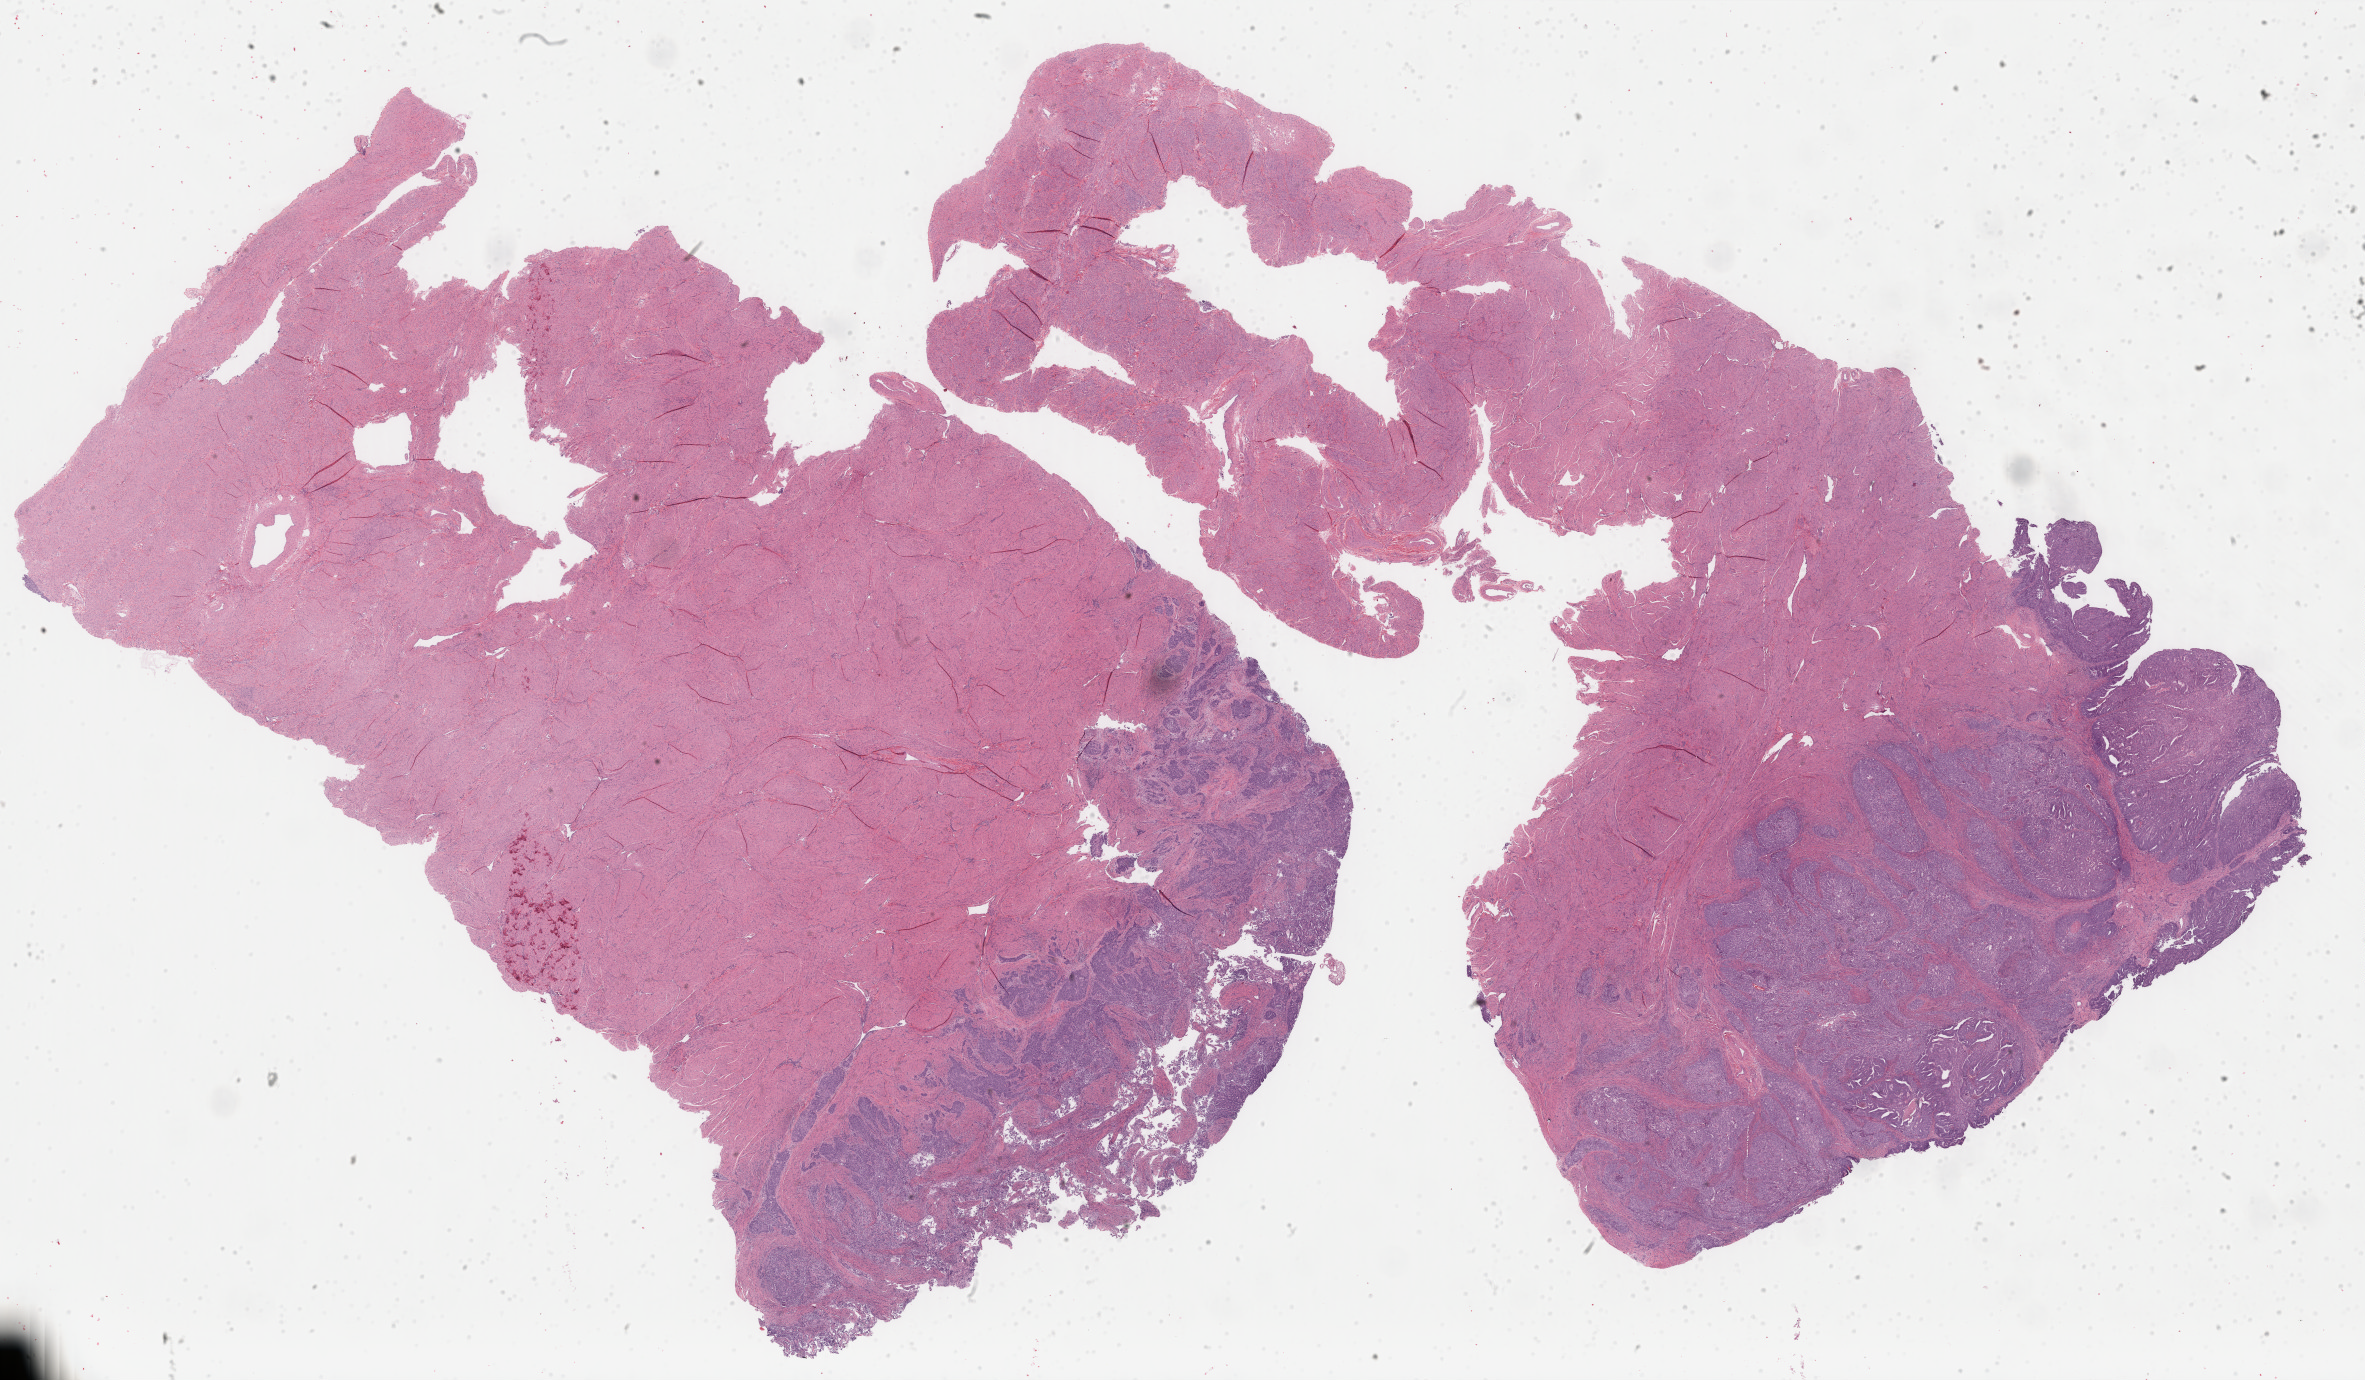
Digitized H&E tissue section (whole slide), a low-resolution overview of the entire scanned area, about 37.5 x 21.9 mm (from a 40x scan); formalin-fixed paraffin-embedded (FFPE) diagnostic section; uterus, primary tumour sample. Female patient; age at initial diagnosis 50 years. Histologic grade: G3 (poorly differentiated).
Diagnosis: Endometrioid adenocarcinoma, NOS (endometrium). Lymph nodes positive (case pathology): 1 of 37 examined. FIGO stage: IB.